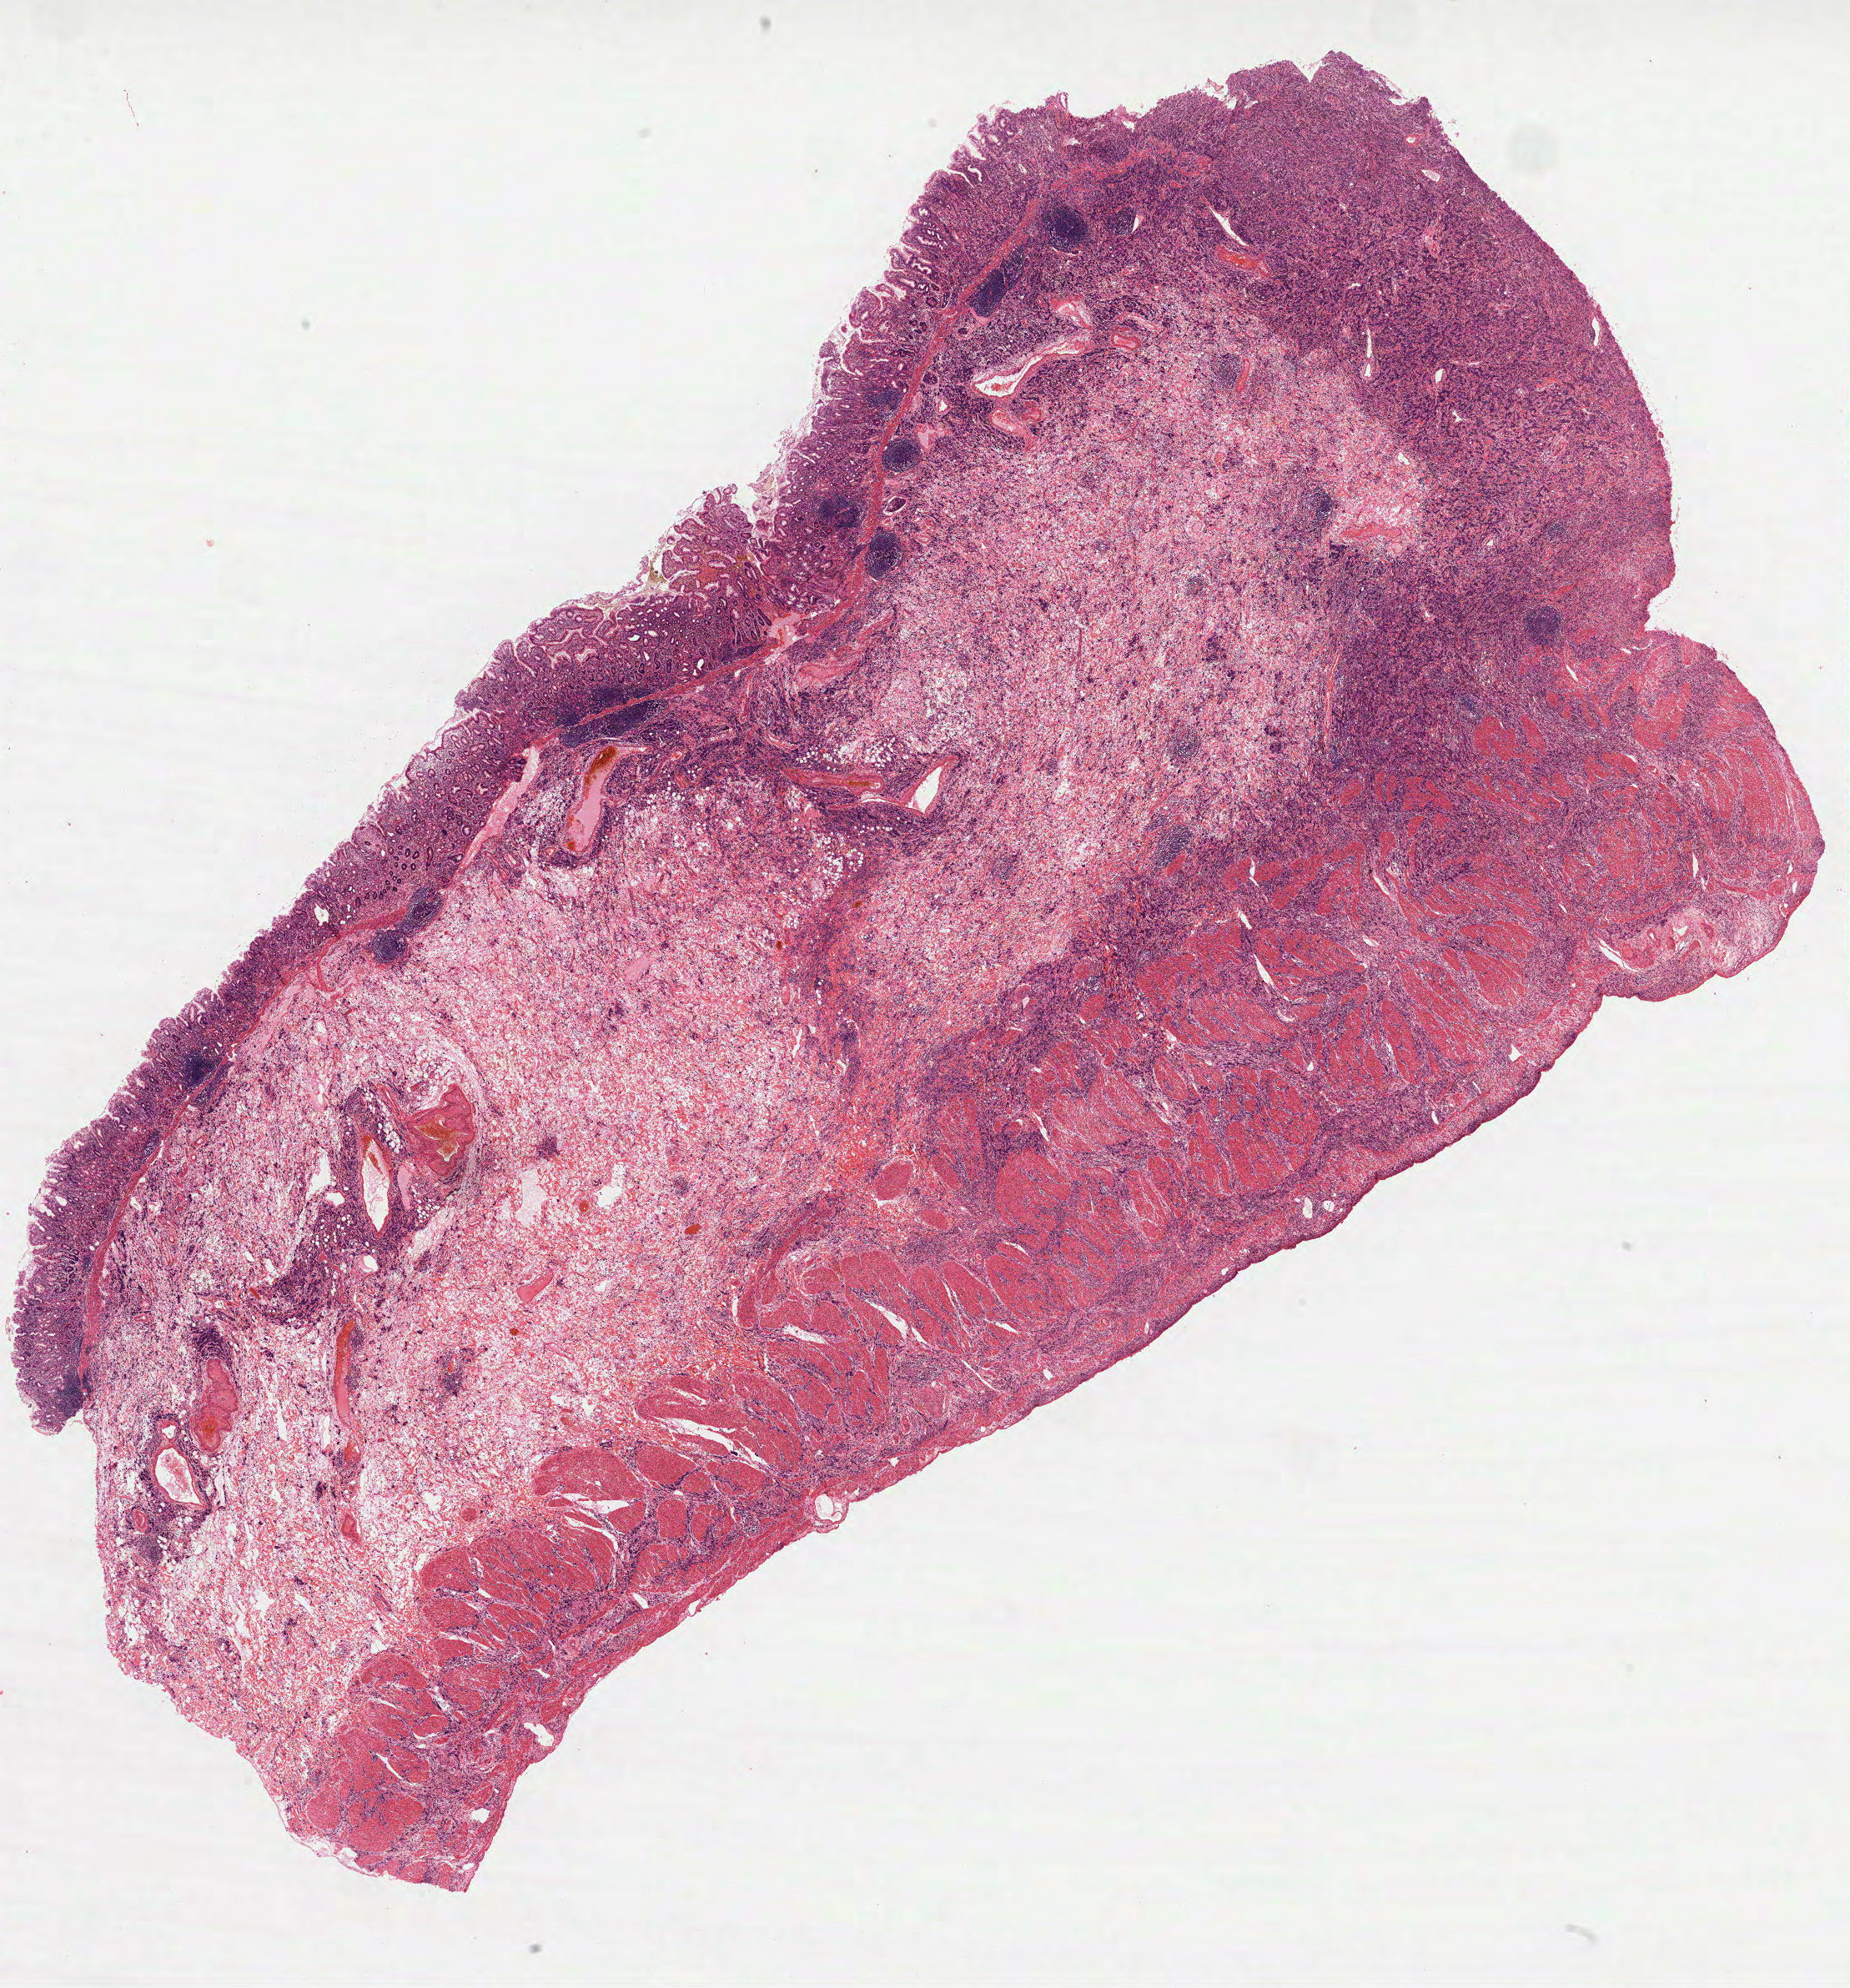
Digitized H&E-stained tissue section (whole slide), a low-resolution overview of the entire scanned area, about 17.9 x 19.2 mm (from a 40x scan), formalin-fixed paraffin-embedded (FFPE) diagnostic section, stomach, primary tumour sample. Patient: male, age at initial diagnosis 69 years. Histologic grade: G3 (poorly differentiated).
• AJCC pathologic stage: IIIB
• histologic diagnosis: Tubular adenocarcinoma (gastric antrum)